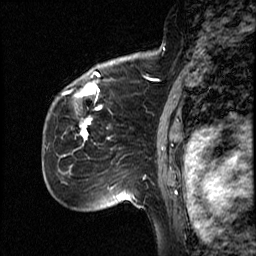
Breast MRI (dynamic contrast-enhanced), one sagittal slice. Position 37 of 50 along the scan axis. Dynamic contrast-enhanced study with each time point stored as its own series, time point 2 of 4 at this slice position (early post-contrast, ordered by acquisition time). 1.5 T. TE 4.2 ms, TR 18.5 ms. 3 mm slice thickness. 256 × 256 image matrix. Patient: female, 44 years. From the clinical record (not read from this slice): setting: breast cancer imaged before/during neoadjuvant chemotherapy; receptor status: HR-positive, HER2-negative.
Outlined on this slice (semi-automatically segmented with operator editing):
- analysis volume of interest (the breast-tissue region the enhancement analysis was run in; not a lesion): bounding box [x1, y1, x2, y2] px = [59, 83, 114, 206]
- tumour enhancement mask (voxels above the 100 % enhancement threshold inside the analysis volume of interest): [81, 106, 102, 140]